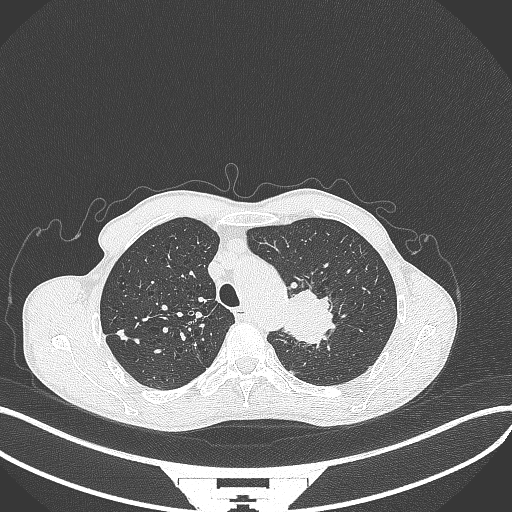
Chest CT, one axial slice. Slice 326 of 386 in the series (ordered by position). Reconstruction kernel B70f. 120 kVp. Lung window (W 1500 / L -600 HU). 1 mm slice thickness. 512 × 512 image matrix, field of view 400 × 400 mm. Male patient, age 65 years. Case-level facts recorded for this patient, not image findings: clinical TNM (as recorded): T2b N0 M0; histopathological grade: G2.
Structures marked on this image (bounding box drawn by a radiologist):
- lung tumour (recorded histology: adenocarcinoma): bounding box (x1, y1, x2, y2) in pixels: (280, 283, 337, 348)